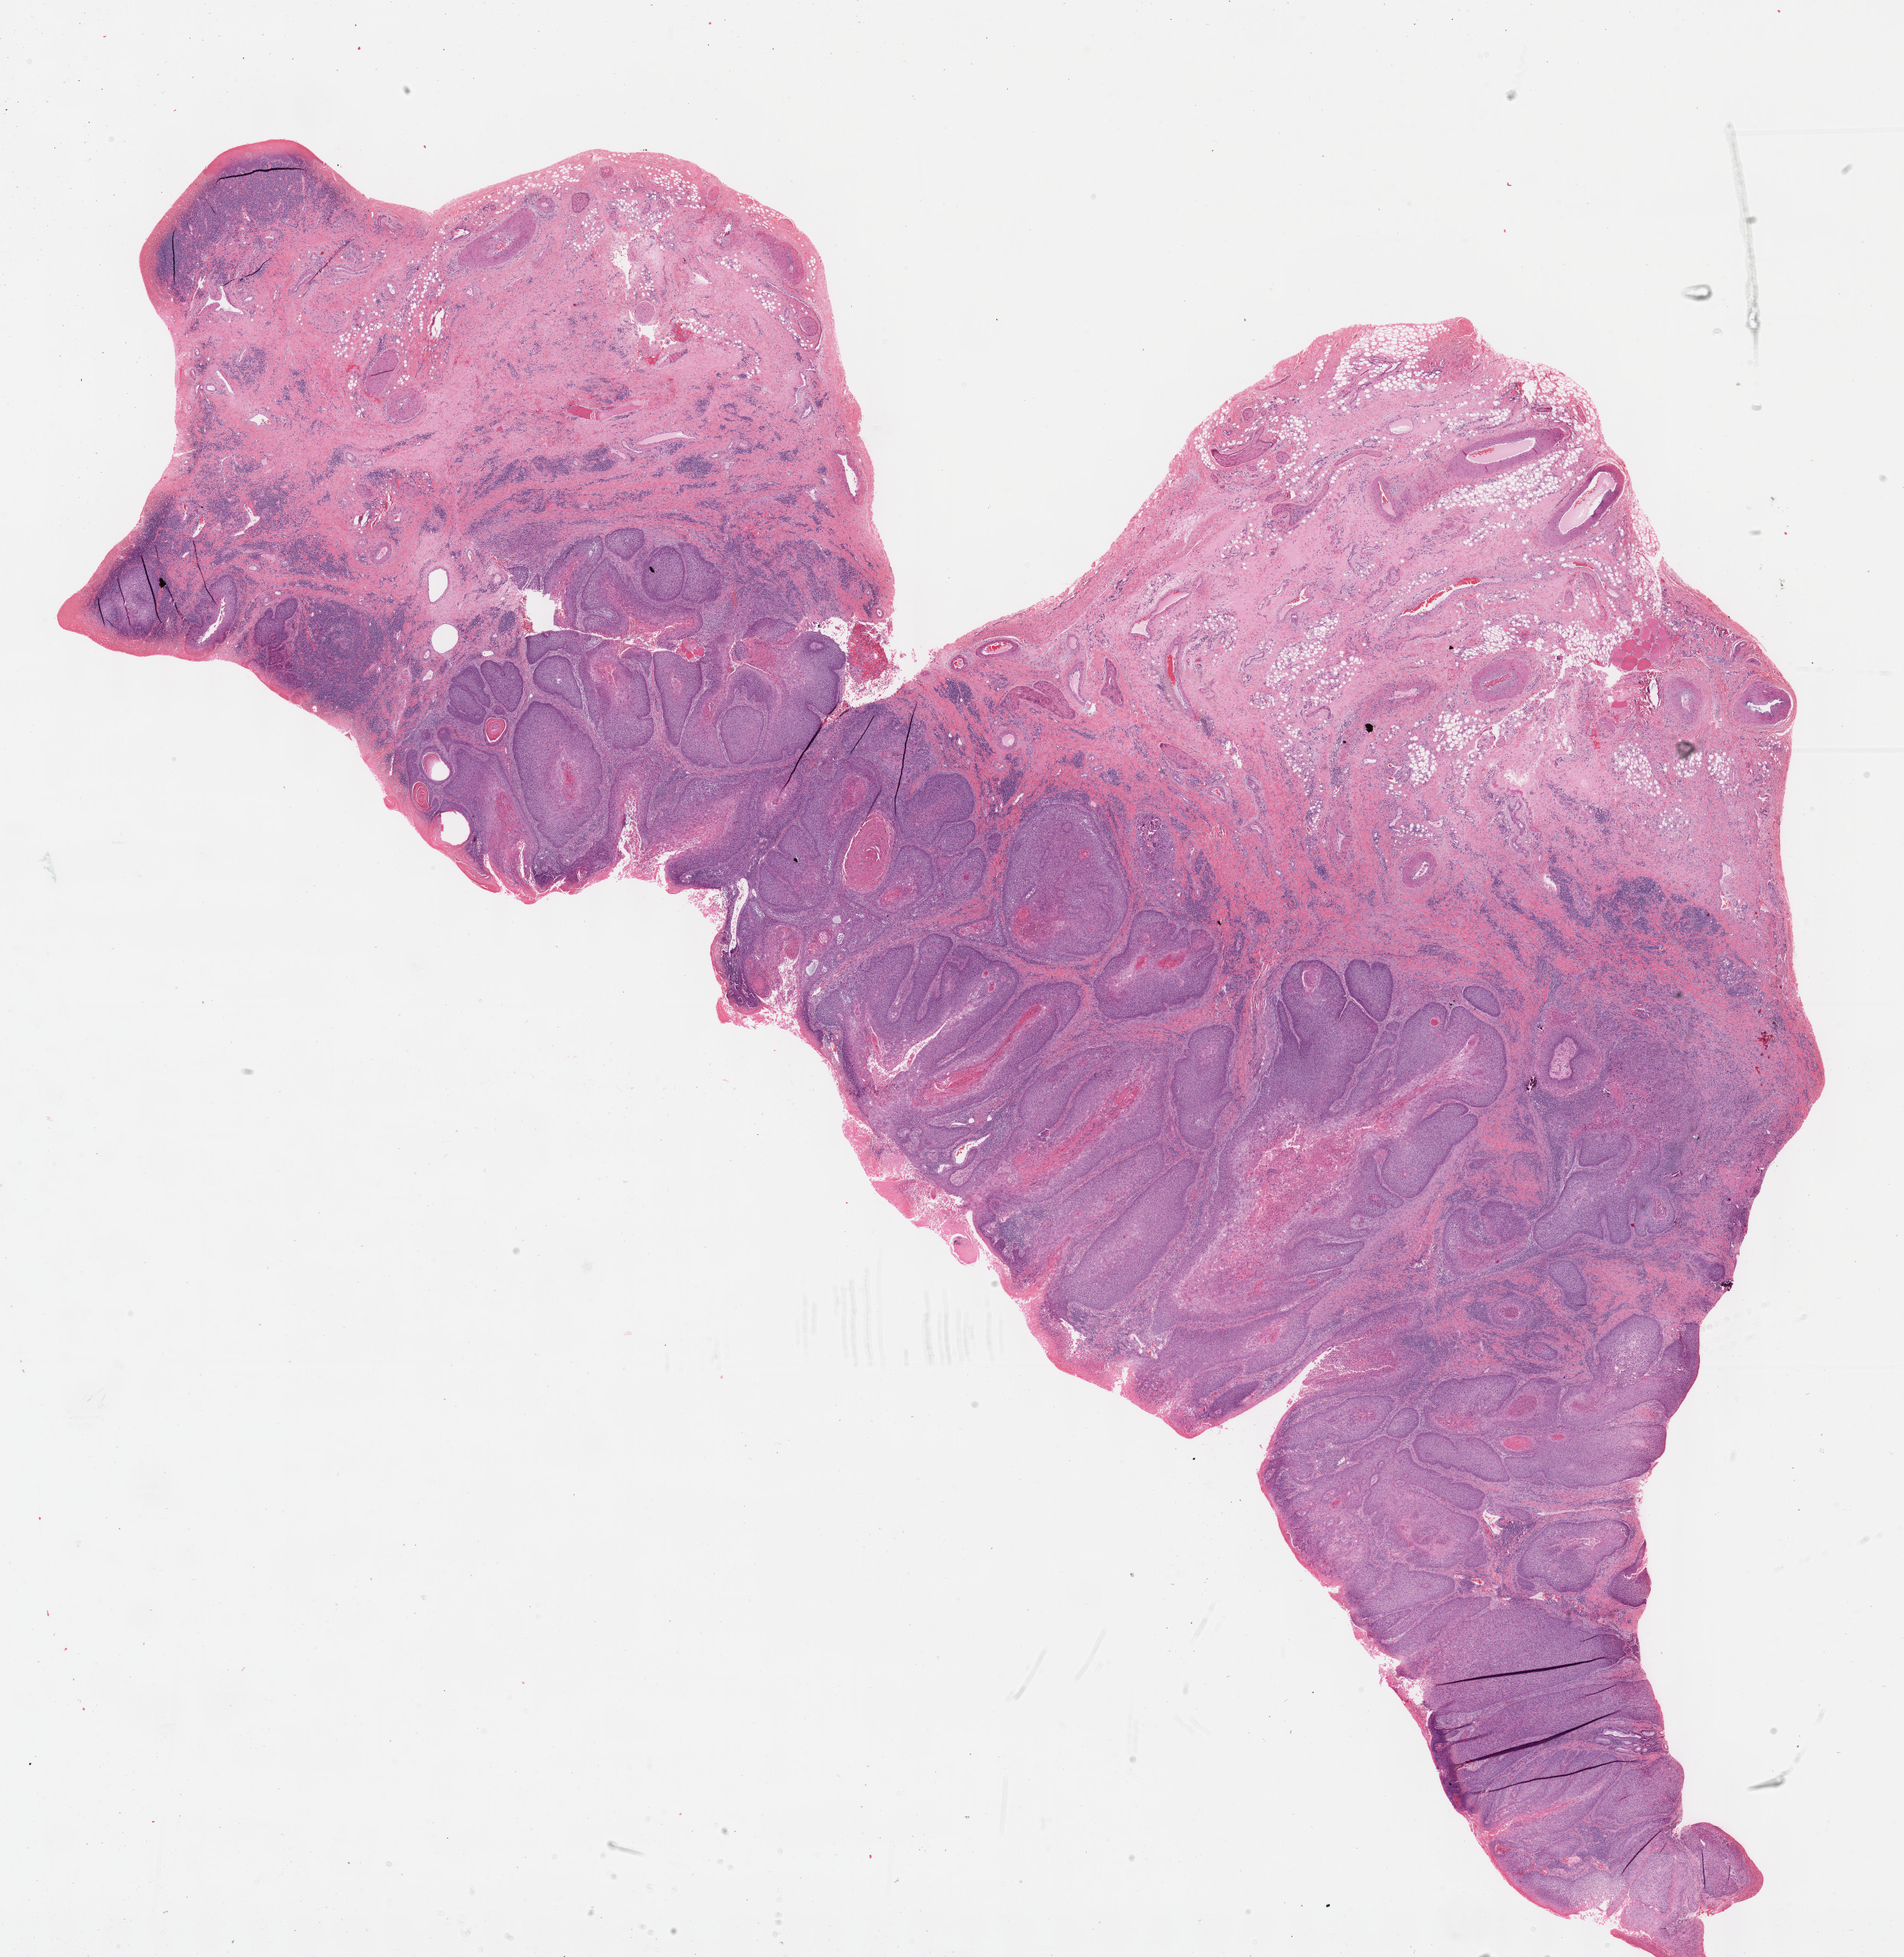
Whole-slide histology image, H&E, low-resolution overview of the scanned area, about 20.1 x 20.7 mm. Formalin-fixed paraffin-embedded (FFPE) diagnostic section. Head and neck, primary tumour sample. Male patient; age at initial diagnosis 64 years. Histologic grade: G1 (well differentiated).
AJCC pathologic stage: IVA (7th edition). Histologic diagnosis: Squamous cell carcinoma, NOS (larynx, NOS). TNM: T4a N0.